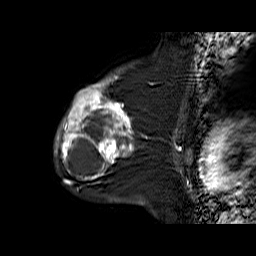
Breast MRI (dynamic contrast-enhanced), one sagittal slice. Slice 45 of 60 in the series (ordered by position). Dynamic contrast-enhanced series, time point 2 of 6 at this slice position (early post-contrast). 1.5 T. TE 6.3 ms, TR 32.9 ms. 256 × 256 image matrix, field of view 200 × 200 mm. Female patient. Case-level facts recorded for this patient, not image findings: setting: breast cancer imaged before/during neoadjuvant chemotherapy; receptor status: triple-negative.
Annotated regions visible in this slice (semi-automatic segmentation, software-assisted and operator-edited):
- analysis volume of interest (the breast-tissue region the enhancement analysis was run in; not a lesion): bounding box <56,76,139,170> (left, top, right, bottom; pixels)
- tumour enhancement mask (voxels above the 100 % enhancement threshold inside the analysis volume of interest): <56,76,134,168>